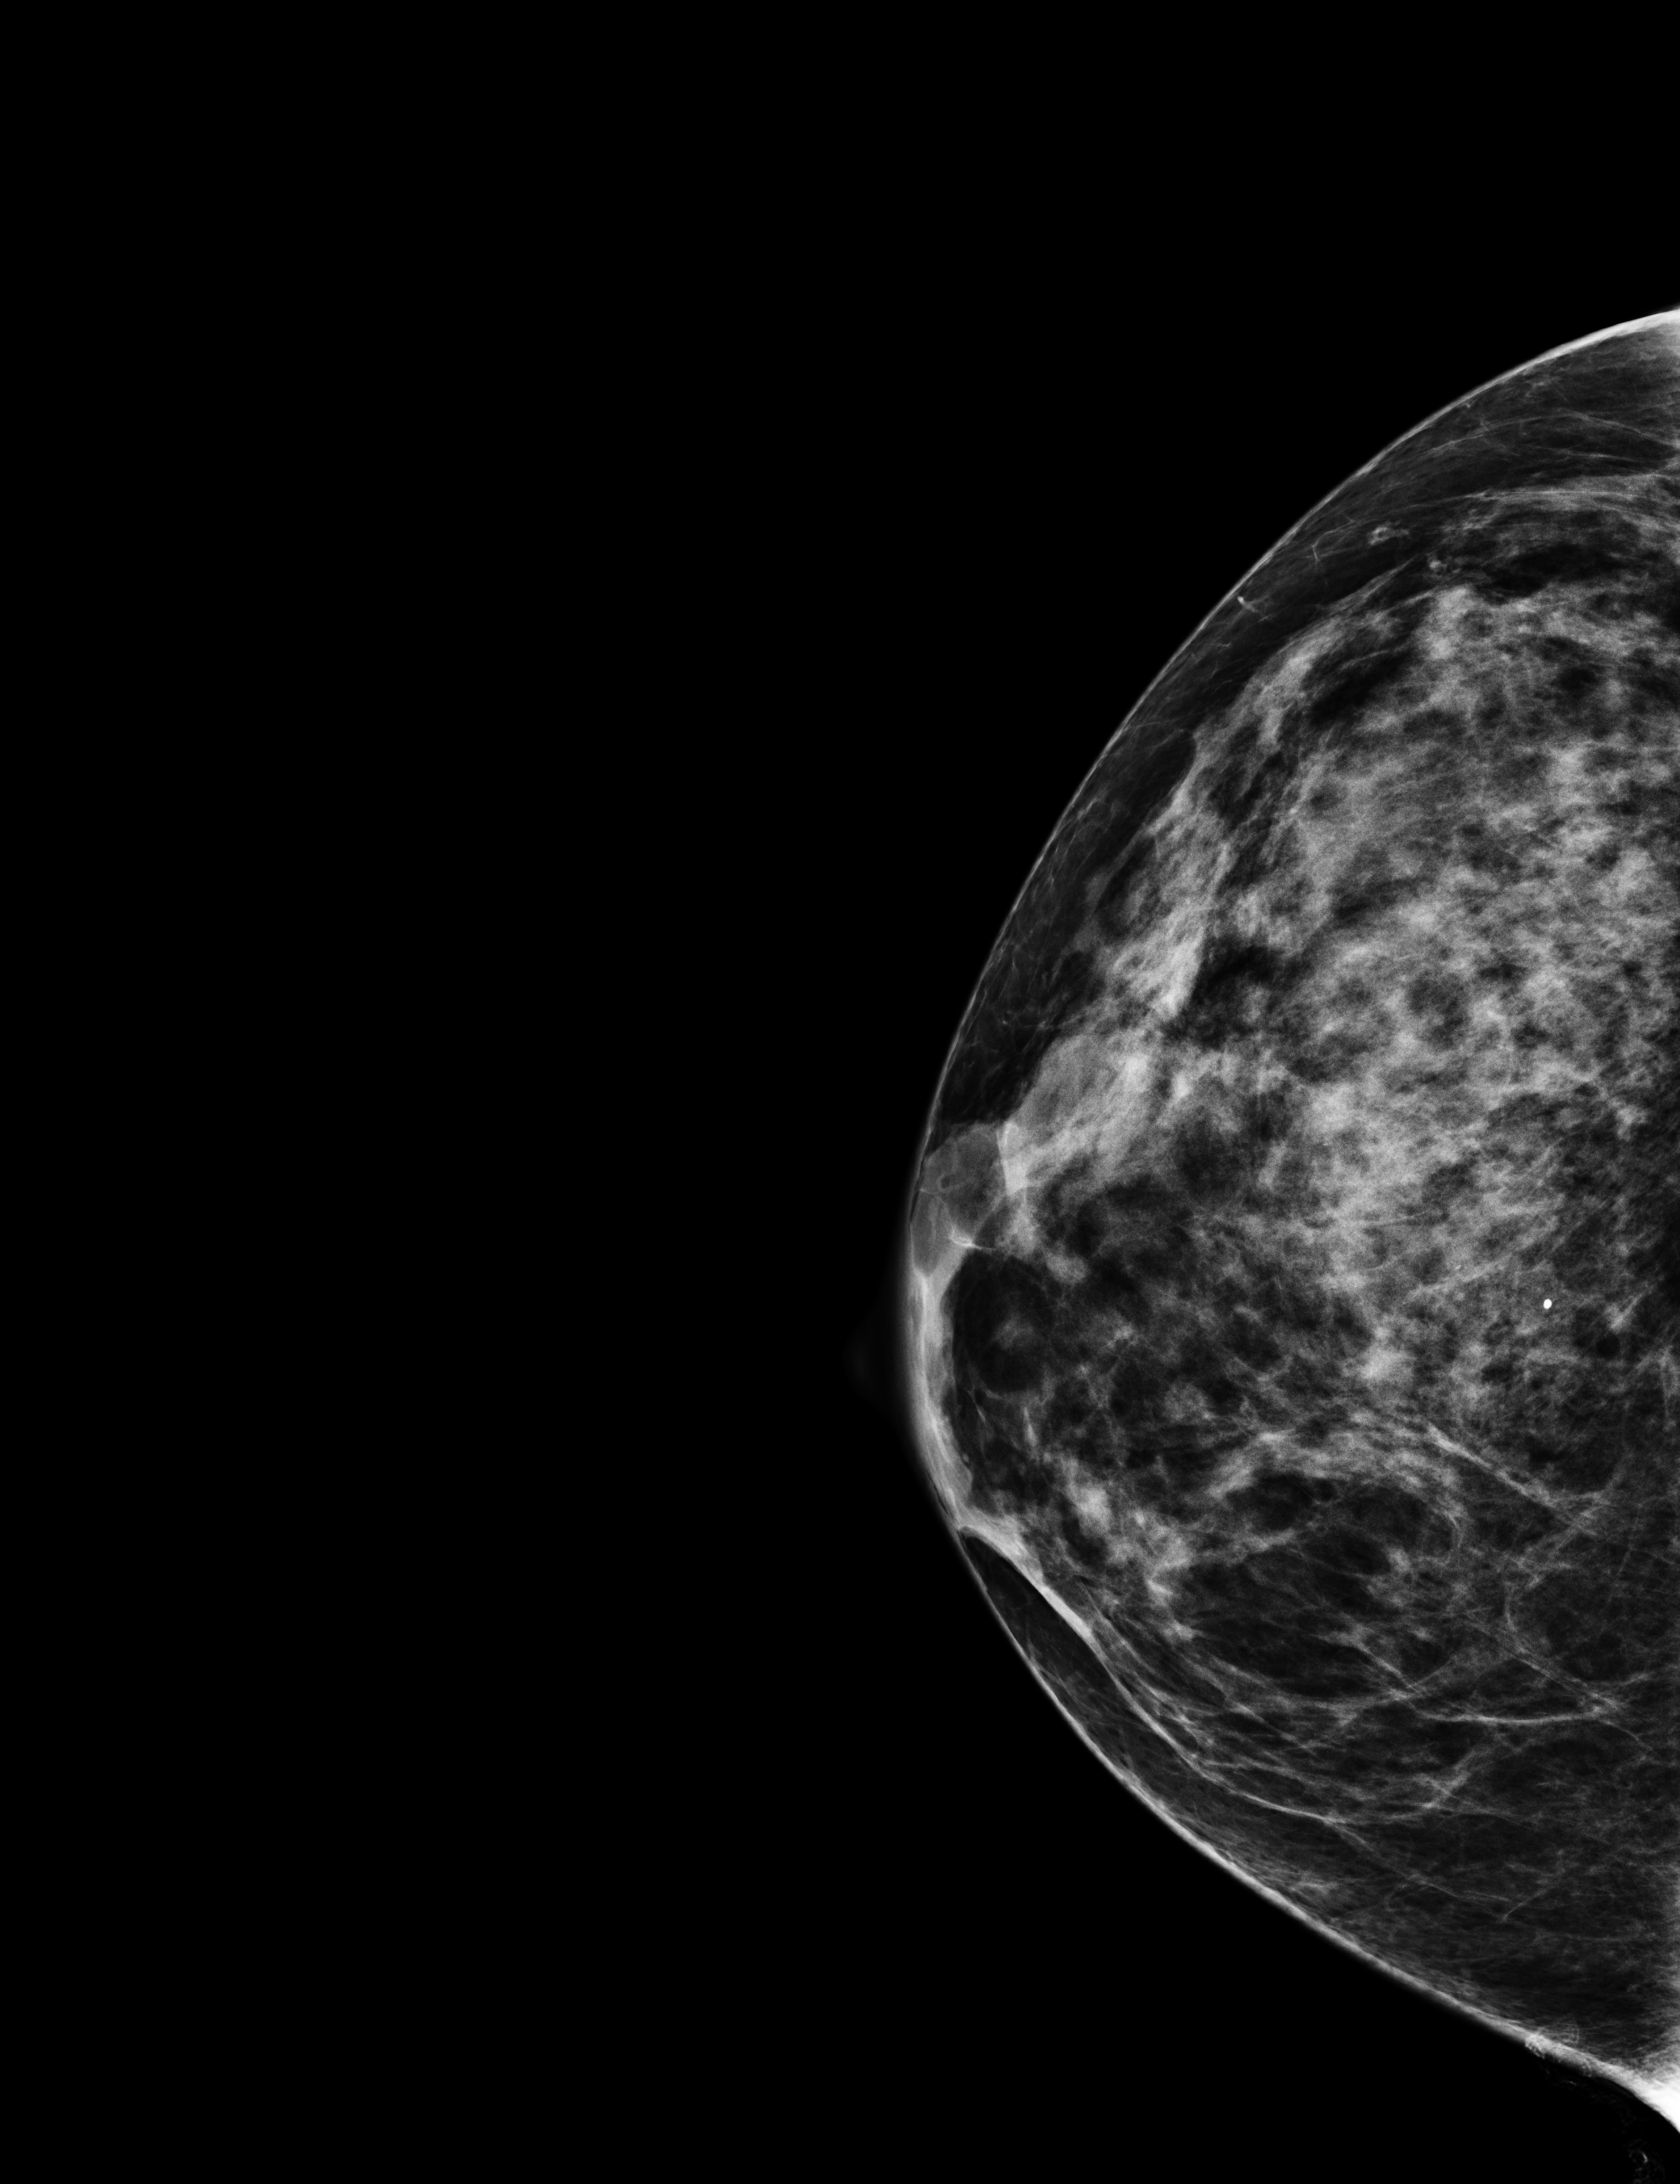
Full-field digital mammogram (FFDM); right breast; CC view; annual screening mammography examination; compressed breast thickness 53 mm; system: Selenia Dimensions. Patient: female, 59 years.
Final BI-RADS assessment for this screening round (tomosynthesis exam, both breasts): category 1.